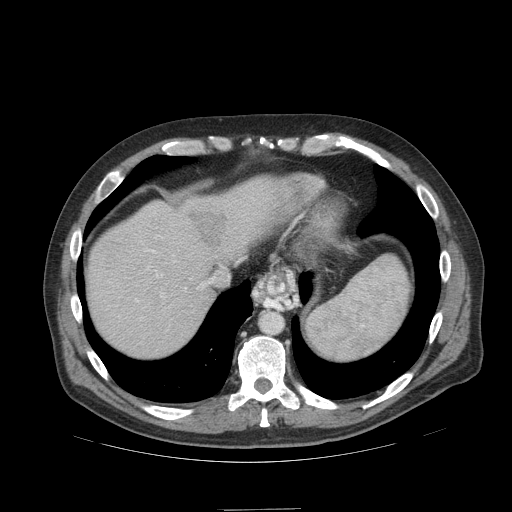
Contrast-enhanced abdominal CT (liver protocol), one axial slice. Slice 86 of 99 in the series (ordered by position). 140 kVp. Soft-tissue window (W 400 / L 40 HU). 2.5 mm slice thickness. 512 × 512 image matrix, field of view 440 × 440 mm. Case-level facts recorded for this patient, not image findings: diagnosis: hepatocellular carcinoma (patient treated with transarterial chemoembolisation; whether this scan precedes or follows treatment is not stated here); TNM stage (as recorded): Stage-I; Child-Pugh class: A; tumour nodularity: uninodular; tumour size: 3.6 cm.
Outlined on this slice (semi-automatic segmentation, software-assisted and operator-edited):
- liver parenchyma outside the tumour (the mass and vessels are separate outlines, so this box may not span the whole liver): bounding box (x1, y1, x2, y2) in pixels: (86, 176, 292, 356)
- mass: (188, 210, 226, 246)
- liver vessels: (136, 235, 203, 302)